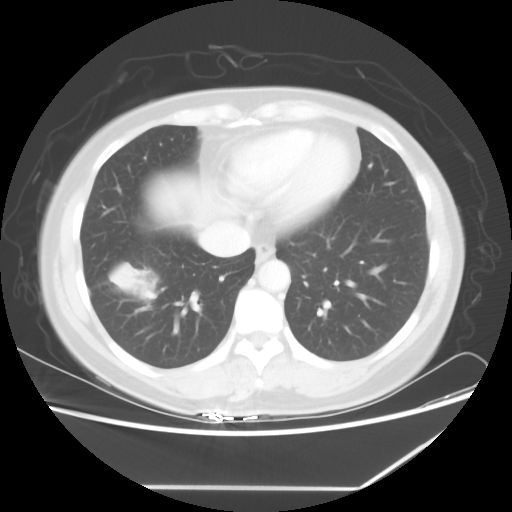
Chest CT, one axial slice; slice 21 of 60 in the series (ordered by position); reconstruction kernel STANDARD; 100 kVp; lung window (W 1500 / L -600 HU); 512 × 512 image matrix, field of view 374 × 374 mm. Patient: female, 42 years. Case-level facts recorded for this patient, not image findings: clinical TNM (as recorded): T2 N1 M0.
Outlined on this slice (rectangle marked by the reading radiologist):
- lung tumour (recorded histology: adenocarcinoma): bounding box [x1, y1, x2, y2] px = [106, 259, 157, 302]